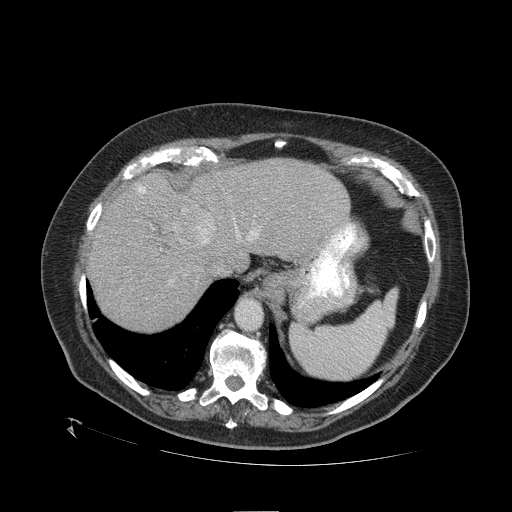
Contrast-enhanced abdominal CT (liver protocol), one axial slice. Slice 86 of 109 in the series (ordered by position). 120 kVp. One of 2 acquisitions stored at this slice position. Soft-tissue window (W 400 / L 40 HU). 2.5 mm slice thickness. 512 × 512 image matrix. Case-level facts recorded for this patient, not image findings: diagnosis: hepatocellular carcinoma (patient treated with transarterial chemoembolisation; whether this scan precedes or follows treatment is not stated here); TNM stage (as recorded): Stage-I; Child-Pugh class: A; tumour differentiation: no biopsy; tumour nodularity: uninodular.
Annotated regions visible in this slice (semi-automatically segmented with operator editing):
- abdominal aorta: bounding box <237,299,262,329> (left, top, right, bottom; pixels)
- liver parenchyma outside the tumour (the mass and vessels are separate outlines, so this box may not span the whole liver): <88,158,350,330>
- mass: <172,204,216,248>
- liver vessels: <138,186,259,241>